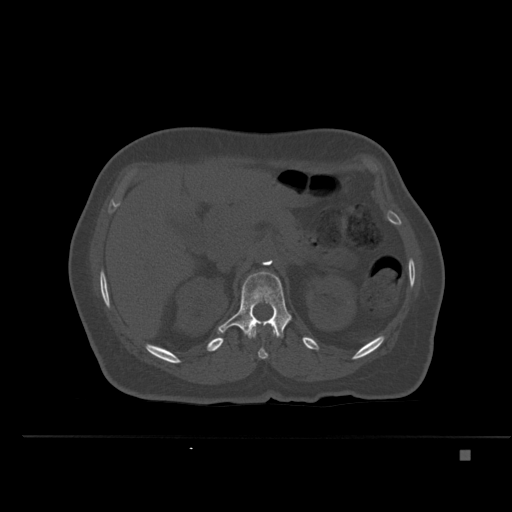
CT including the spine, one axial slice. Position 239 of 477 along the scan axis. Bone window (W 1800 / L 400 HU). 1.5 mm slice thickness. 512 × 512 image matrix, field of view 422 × 422 mm. Patient: female, 74 years. From the clinical record (not read from this slice): primary cancer: colon.
Structures marked on this image (semi-automatic segmentation, software-assisted and operator-edited):
- L1 vertebra: bounding box (x1, y1, x2, y2) in pixels: (218, 271, 292, 338)
- T12 vertebra: (250, 325, 277, 359)